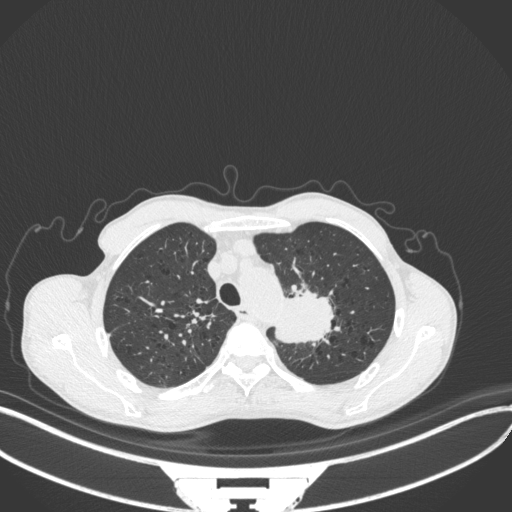
Chest CT, one axial slice. Slice 335 of 394 in the series (ordered by position). Reconstruction kernel B31f. 120 kVp. Lung window (W 1500 / L -600 HU). 1 mm slice thickness. 512 × 512 image matrix. Patient: male, 65 years. Case-level facts recorded for this patient, not image findings: clinical TNM (as recorded): T2b N0 M0.
Structures marked on this image (rectangle marked by the reading radiologist):
- lung tumour (recorded histology: adenocarcinoma): bounding box [x1, y1, x2, y2] px = [270, 290, 337, 343]